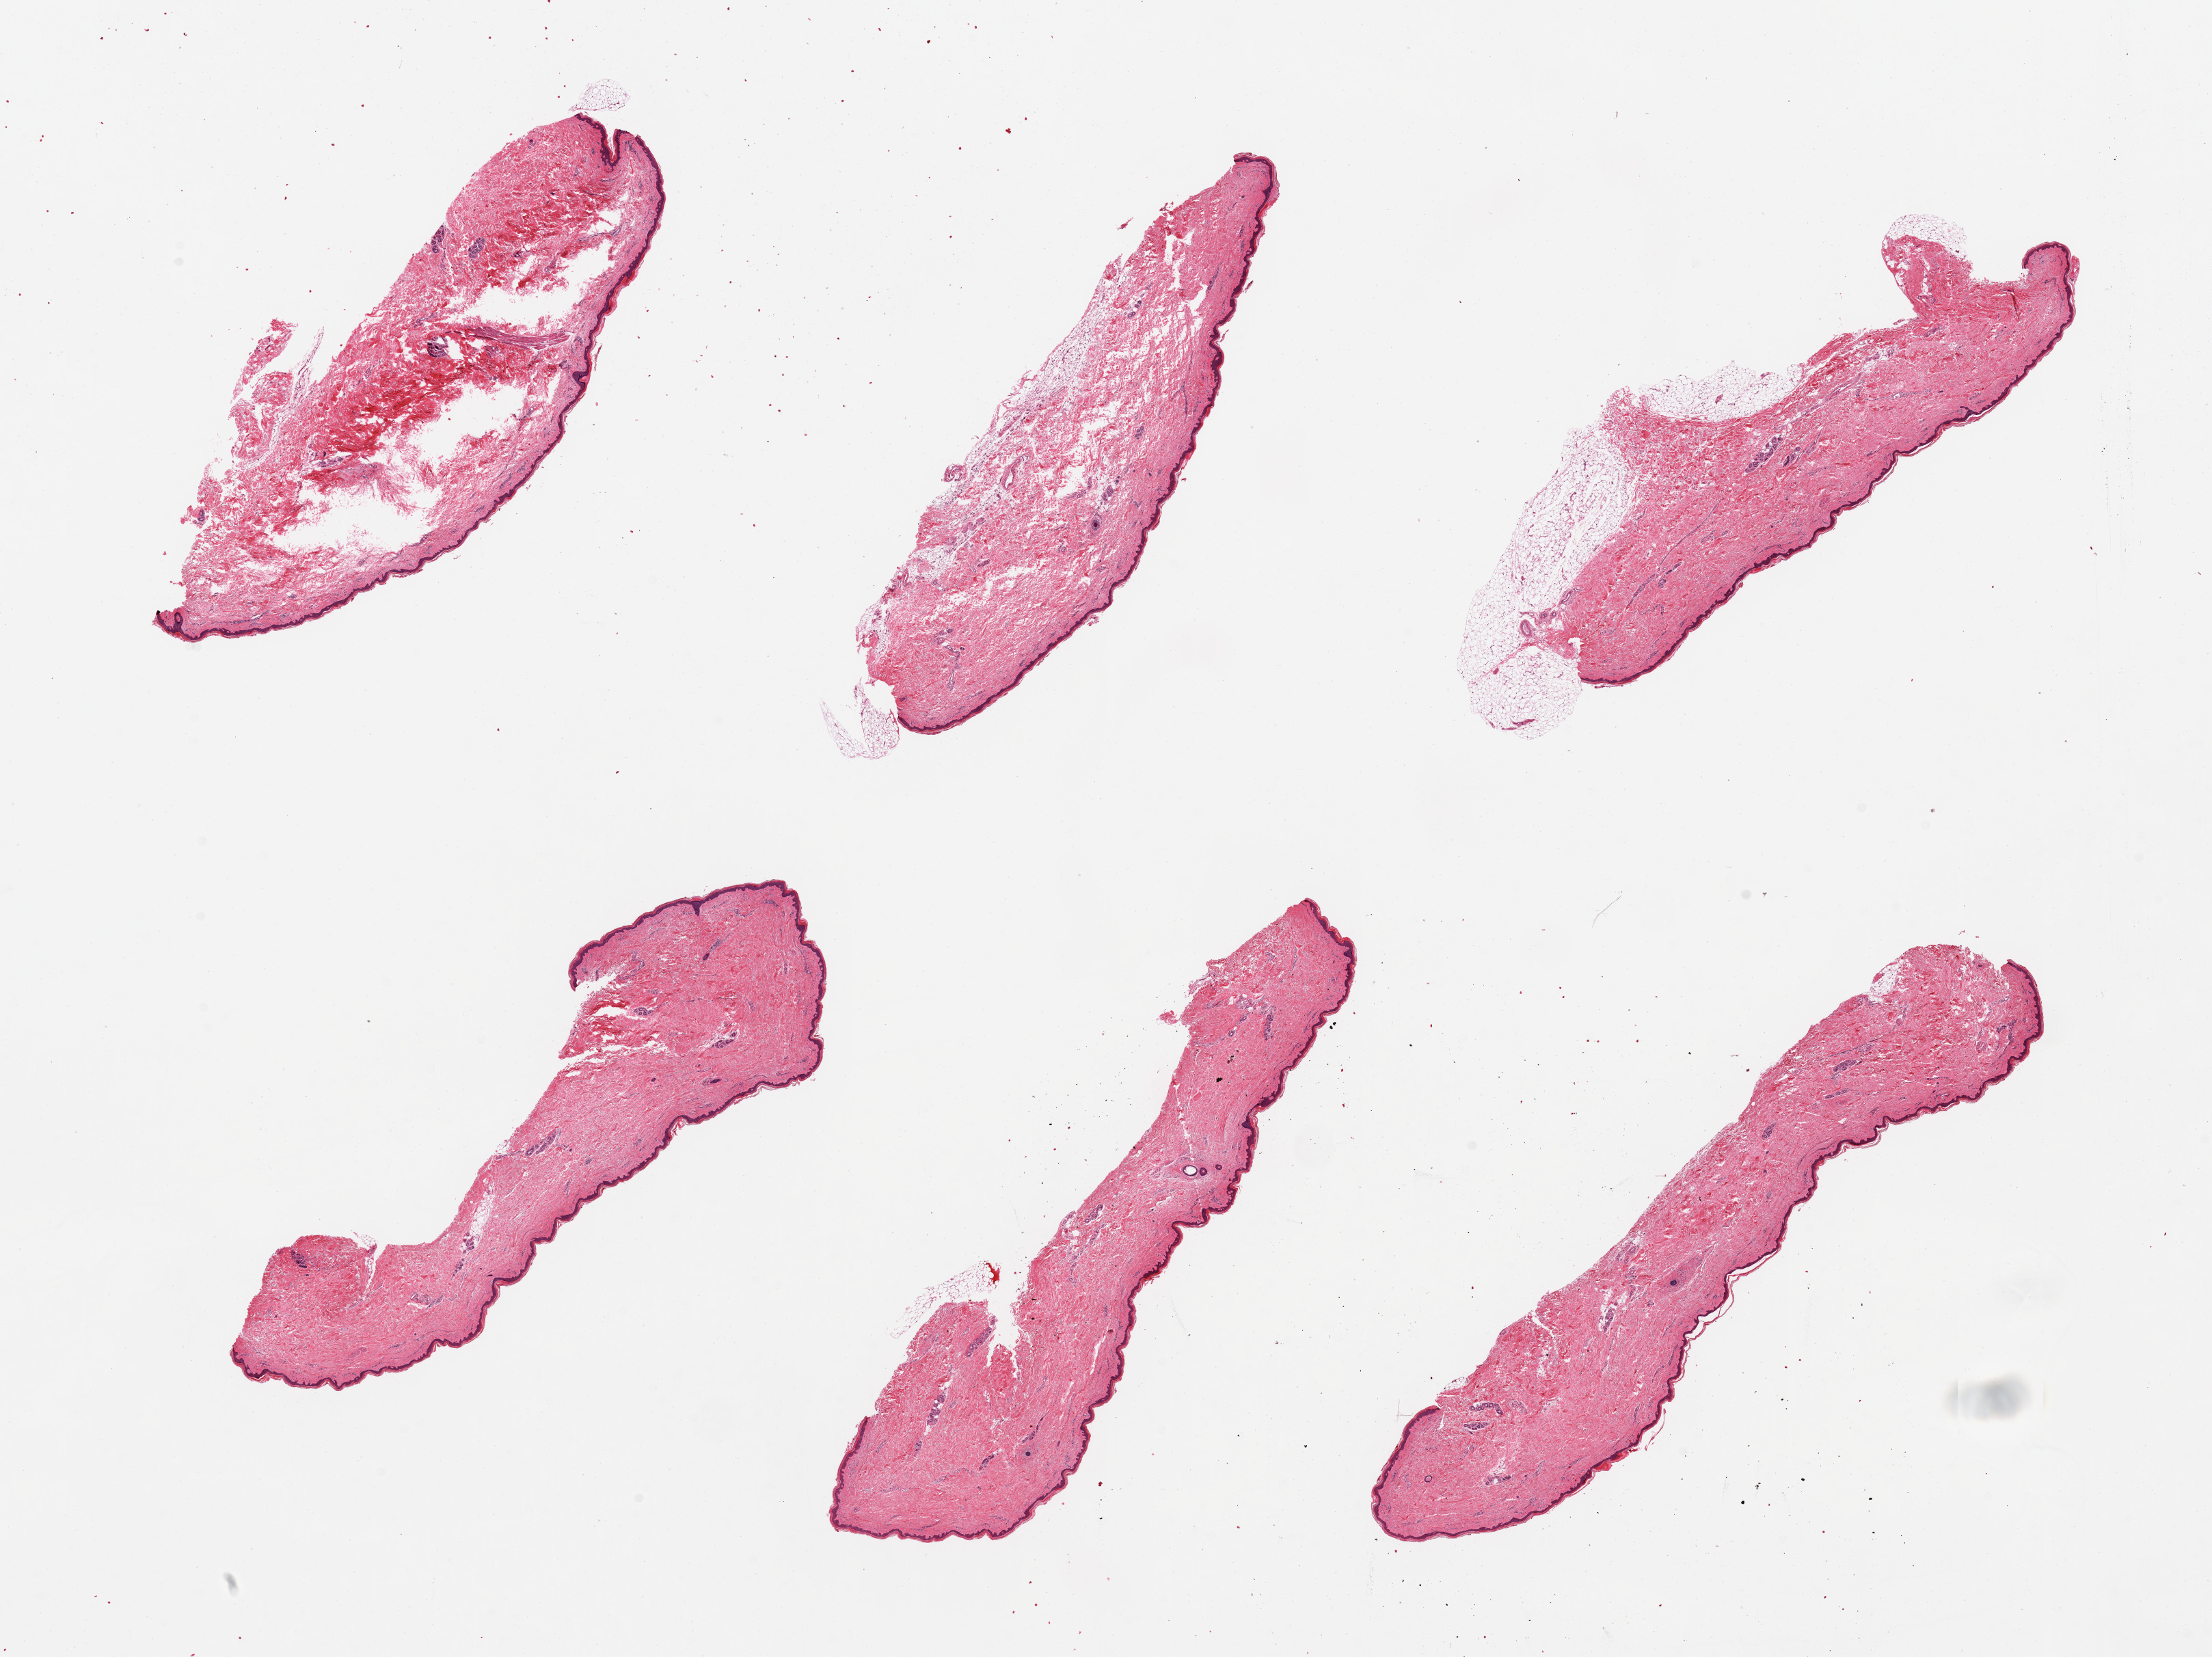
Haematoxylin and eosin whole-slide image, brightfield — whole scanned area (about 25.6 x 19.2 mm) shown as a low-resolution overview, PAXgene-fixed, paraffin-embedded tissue, section of skin of suprapubic region (target tissue), donor tissue sample. Donor: female.
• review note (as recorded): 6 pieces, minimal adherent dermal fat